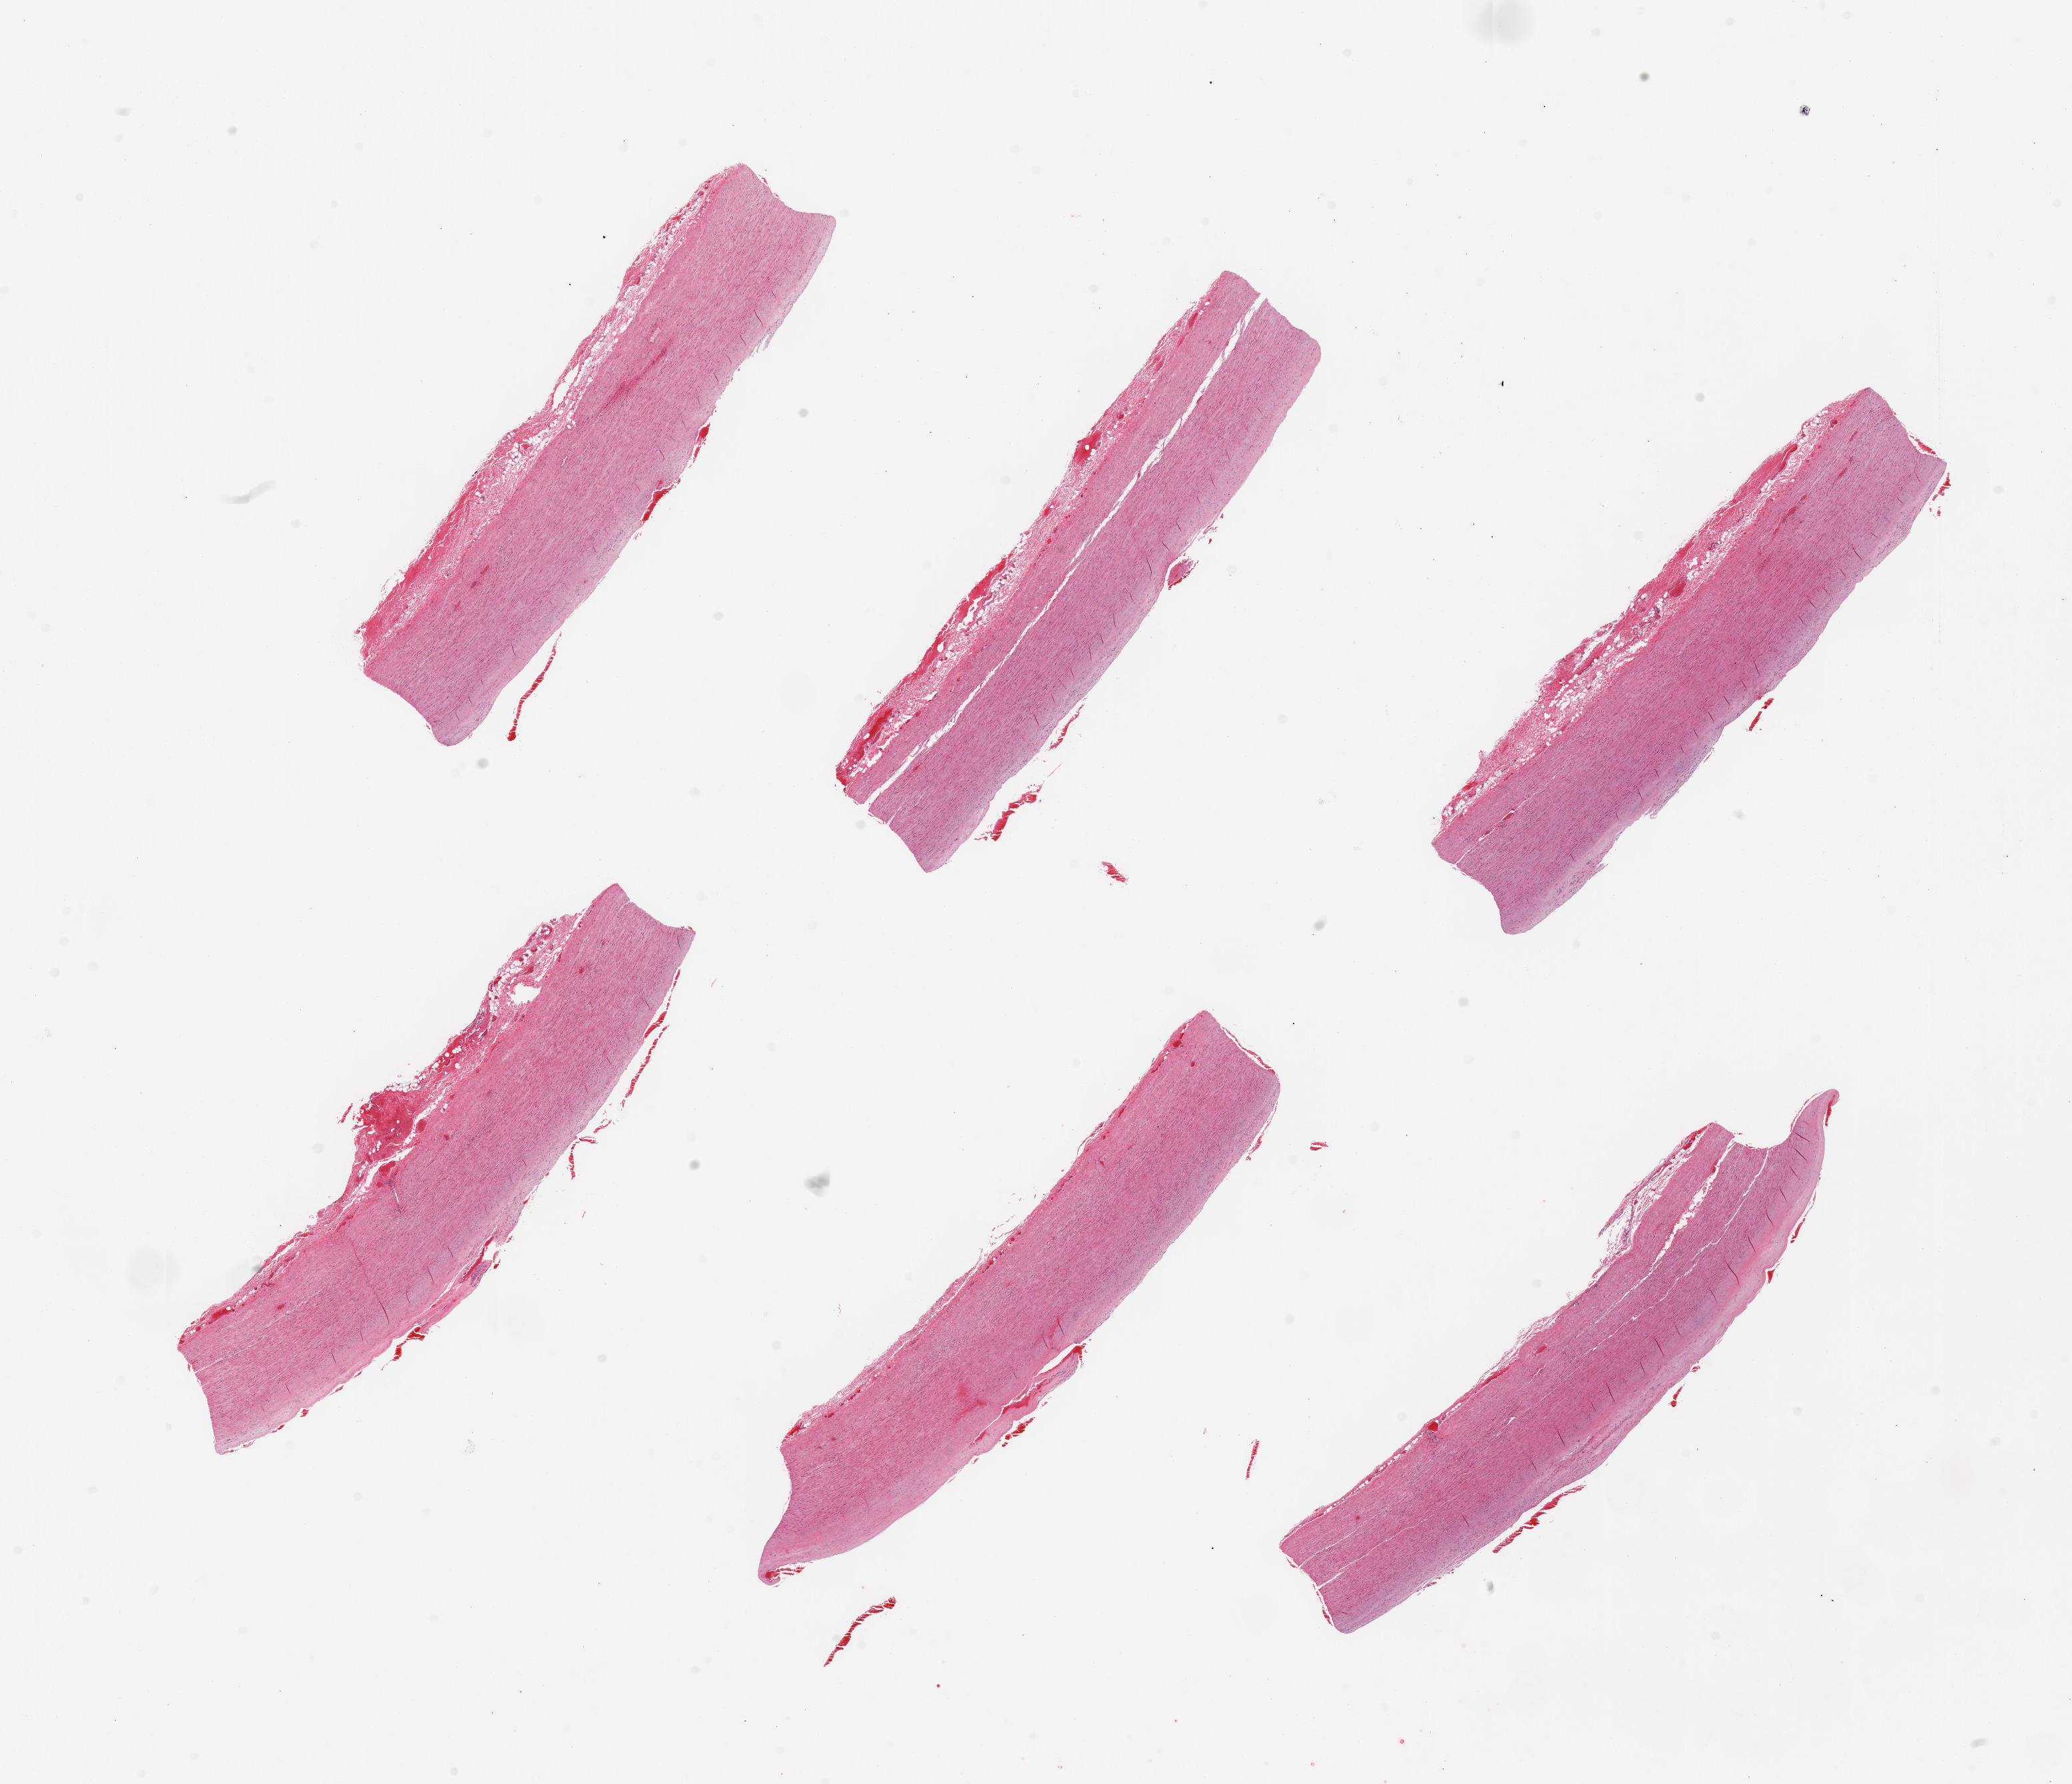
Digitized hematoxylin and eosin (H&E)-stained section, brightfield — whole scanned area (about 24.6 x 21.2 mm, acquisition: 20x scan) shown as a low-resolution overview, PAXgene-fixed, paraffin-embedded tissue, section of aorta (target tissue), tissue donor sample. Donor: male.
- reviewer comment on this tissue sample: 6 pieces; atherosclerosis